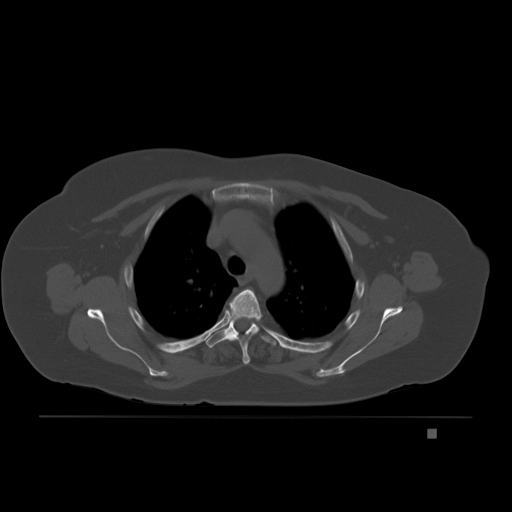
CT including the spine, one axial slice. Bone window (W 1800 / L 400 HU). 3 mm slice thickness. 512 × 512 image matrix, field of view 474 × 474 mm. Patient: female, 63 years. Case-level facts recorded for this patient, not image findings: primary cancer: breast.
Outlined on this slice (semi-automatically segmented with operator editing):
- T3 vertebra: bounding box (x1, y1, x2, y2) in pixels: (230, 290, 261, 364)
- T4 vertebra: (206, 321, 277, 348)